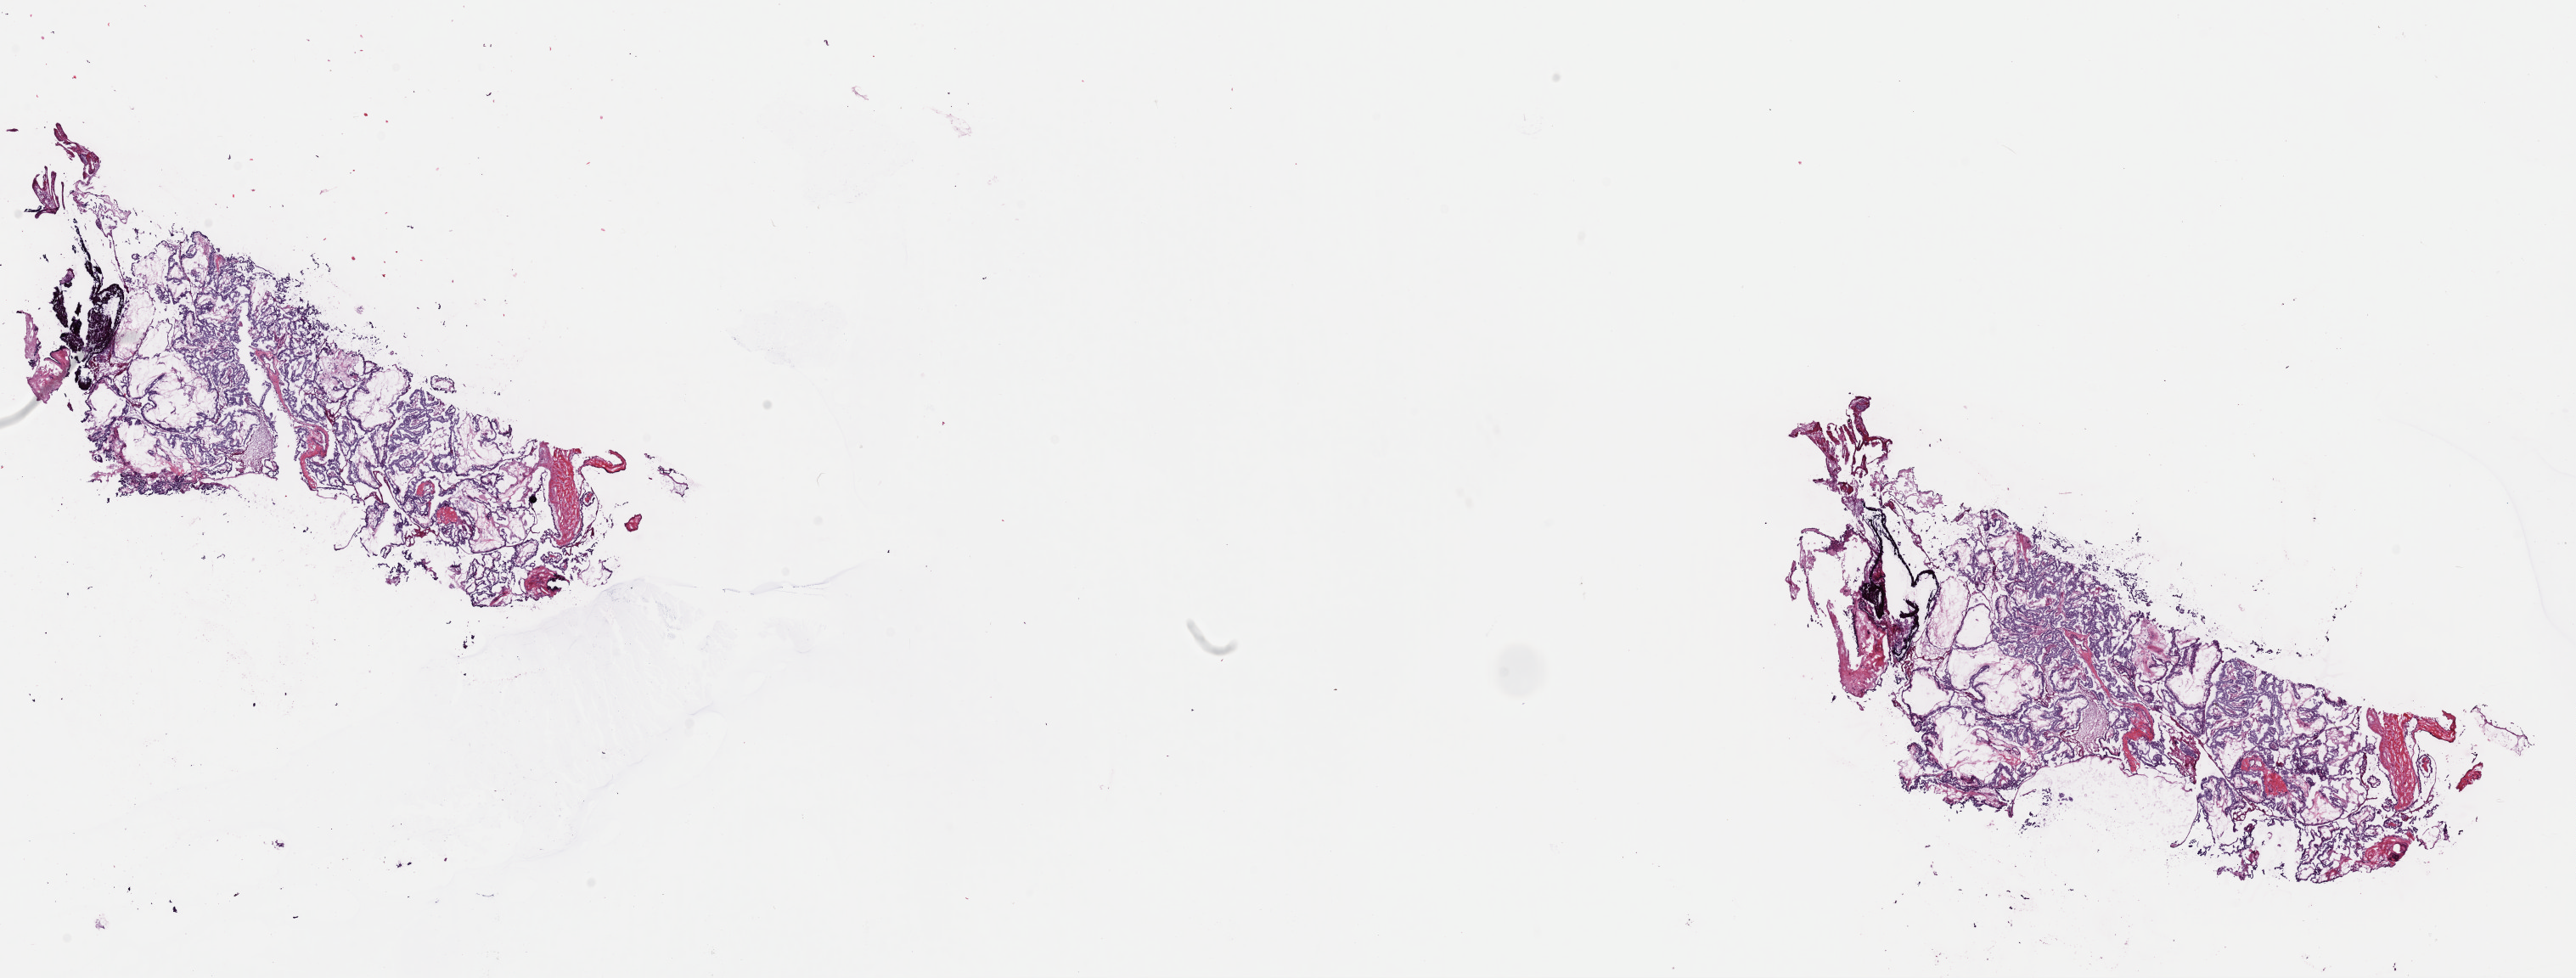
Hematoxylin and eosin (H&E) stained whole-slide image, low-resolution overview of the scanned area, about 24.0 x 9.1 mm (slide scanned at 40x); frozen section; thyroid, primary tumour sample. Patient: female, age at initial diagnosis 28 years. Pathologist review of this section (percent, as recorded): tumour cells 95%, tumour nuclei 85%, normal cells 0%, stromal cells 5%, necrosis 0%. Inflammatory infiltration, as recorded: lymphocyte infiltration 0%, monocyte infiltration 0%, neutrophil infiltration 0%.
* AJCC pathologic stage: I (6th edition)
* lymph nodes positive (case pathology): 1 of 8 examined
* histologic diagnosis: Papillary adenocarcinoma, NOS (thyroid gland)